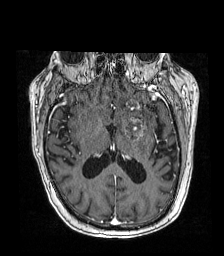
Brain MRI from a brain-tumour surgery series, one axial slice. Position 86 of 192 along the scan axis. T1-weighted post-contrast. 224 × 256 image matrix. Case-level facts recorded for this patient, not image findings: histopathology: Metastatic carcinoma from lung primary.
Annotated regions visible in this slice (manually delineated by an expert):
- tumour: bounding box [x1, y1, x2, y2] px = [117, 115, 148, 139]